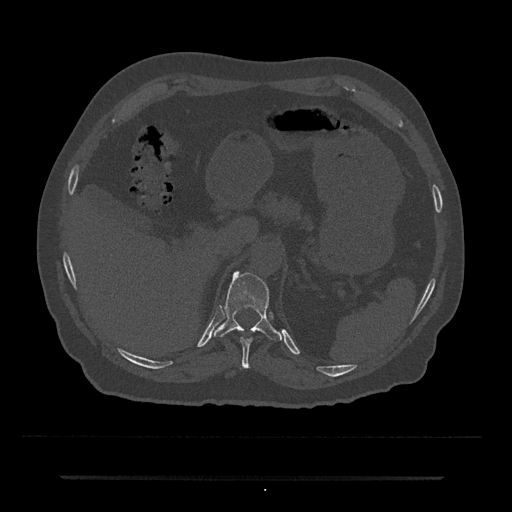
CT including the spine, one axial slice; slice 192 of 797 in the series (ordered by position); reconstruction kernel Br40s/3; 120 kVp; bone window (W 1800 / L 400 HU); 0.5 mm slice thickness; 512 × 512 image matrix. Male patient, age 69 years. Case-level facts recorded for this patient, not image findings: primary cancer: prostate.
Structures marked on this image (semi-automatic segmentation, software-assisted and operator-edited):
- T10 vertebra: bounding box (x1, y1, x2, y2) in pixels: (240, 337, 253, 368)
- T11 vertebra: (214, 272, 283, 341)